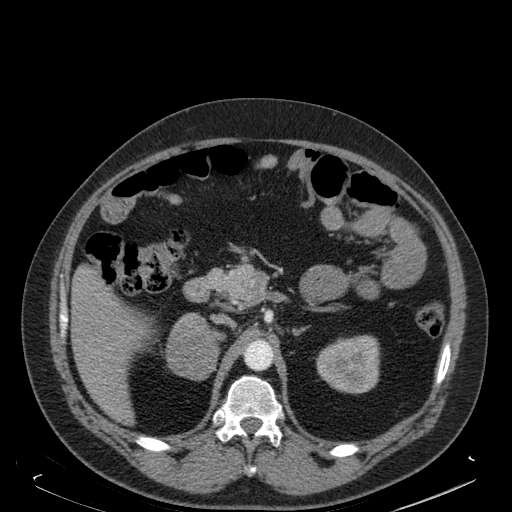
Contrast-enhanced abdominal CT, one axial slice; position 109 of 181 along the scan axis; soft-tissue window (W 400 / L 40 HU); 512 × 512 image matrix. Male patient. Case-level facts recorded for this patient, not image findings: diagnosis: adrenocortical carcinoma; tumour side: right adrenal; tumour size at pathology: 7.5 cm; Ki-67 index: 25 %; stage (as recorded): 4.
Outlined on this slice (semi-automatic segmentation, software-assisted and operator-edited):
- mass: bounding box [x1, y1, x2, y2] px = [167, 315, 216, 377]